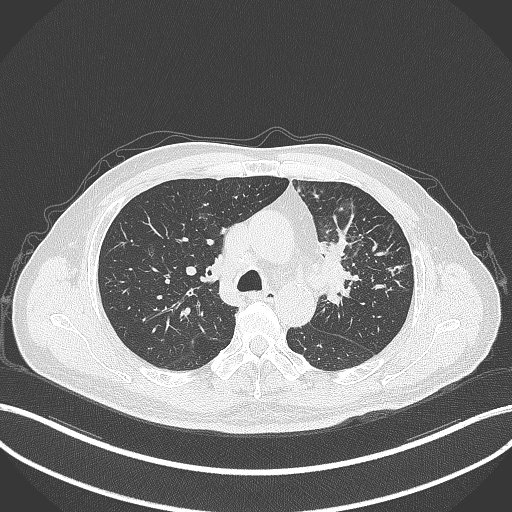
Chest CT, one axial slice. Position 235 of 386 along the scan axis. 120 kVp. Lung window (W 1500 / L -600 HU). 512 × 512 image matrix, field of view 400 × 400 mm. Patient: male, 69 years. From the clinical record (not read from this slice): clinical TNM (as recorded): T2a N2 M0; histopathological grade: G2-3.
Annotated regions visible in this slice (rectangle marked by the reading radiologist):
- lung tumour (recorded histology: adenocarcinoma): bounding box (x1, y1, x2, y2) in pixels: (320, 235, 358, 314)